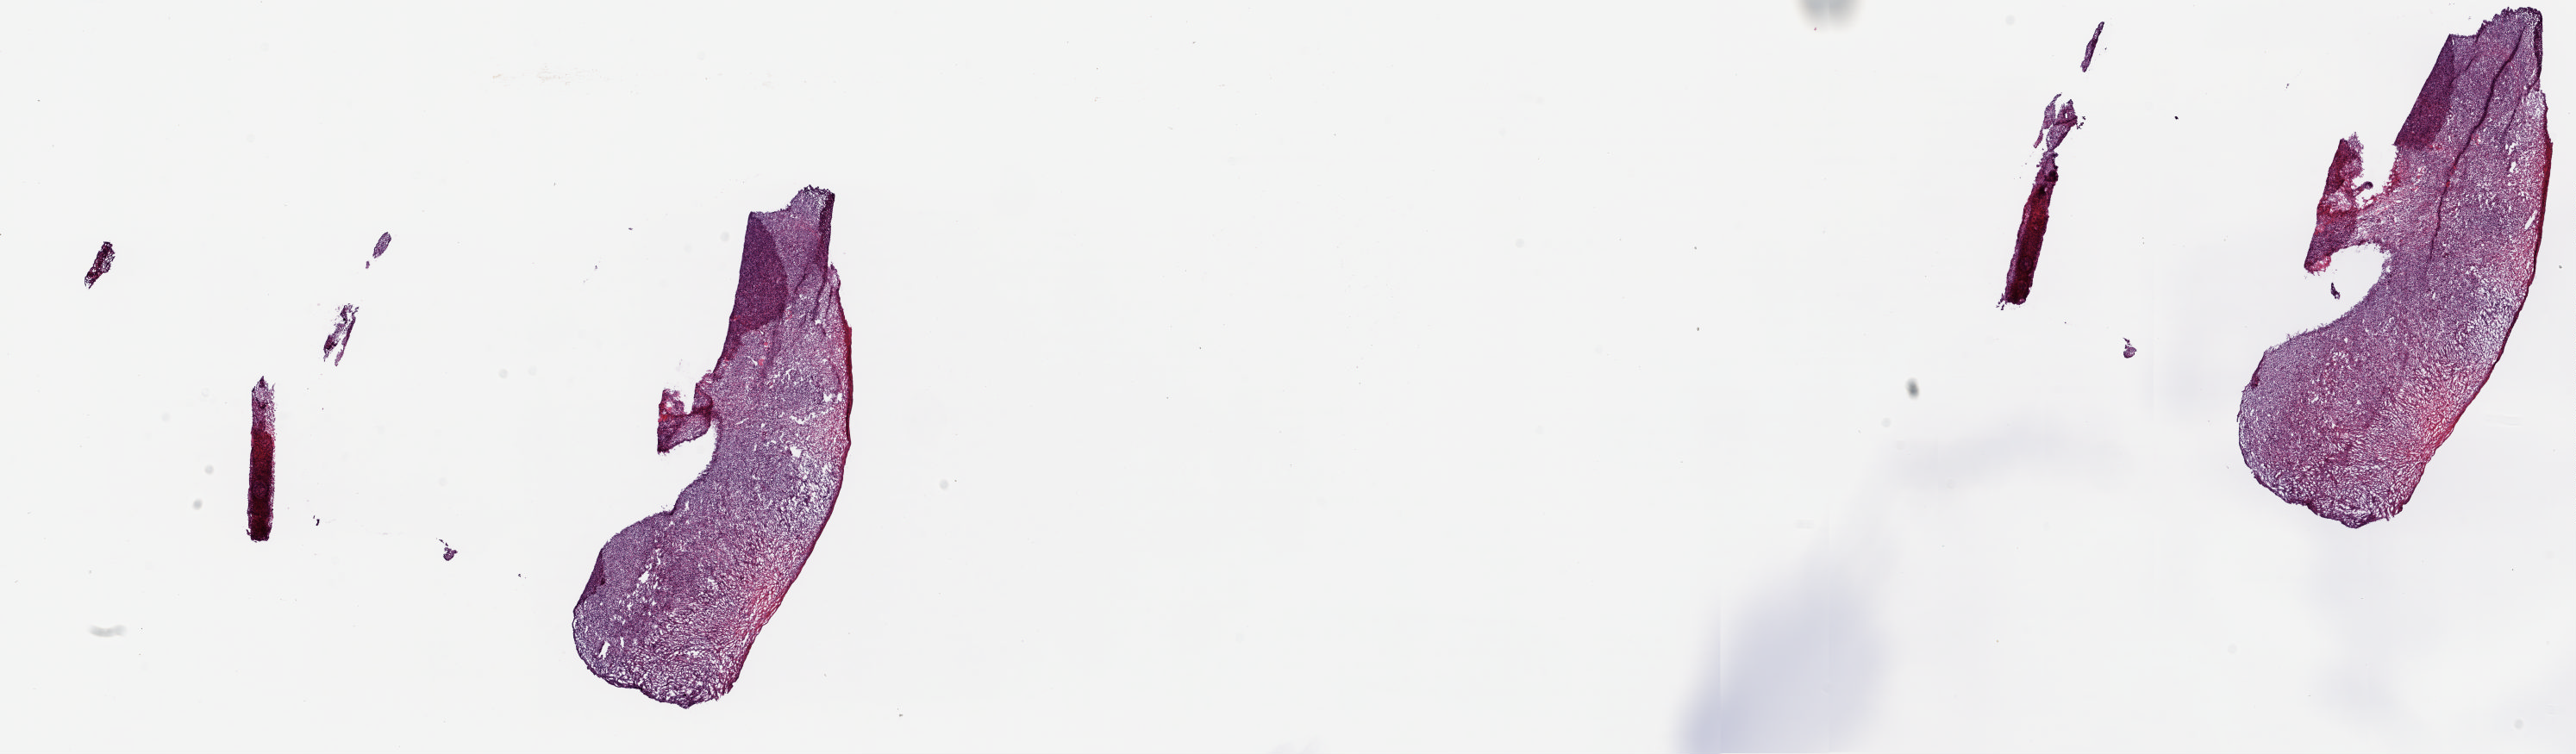
Whole-slide histology image, H&E — shown as a low-resolution overview of the whole scanned area (about 23.7 x 7.0 mm, slide scanned at 20x). Frozen section from the top of the tissue portion. Solid tissue normal (non-tumour tissue) sample from the uterus. Patient: female, age at initial diagnosis 56 years. Composition of this section per pathologist review: tumour cells 0%, tumour nuclei 0%.
This section: solid tissue normal sample (biorepository sample class). Patient diagnosis: Endometrioid adenocarcinoma, NOS (endometrium).